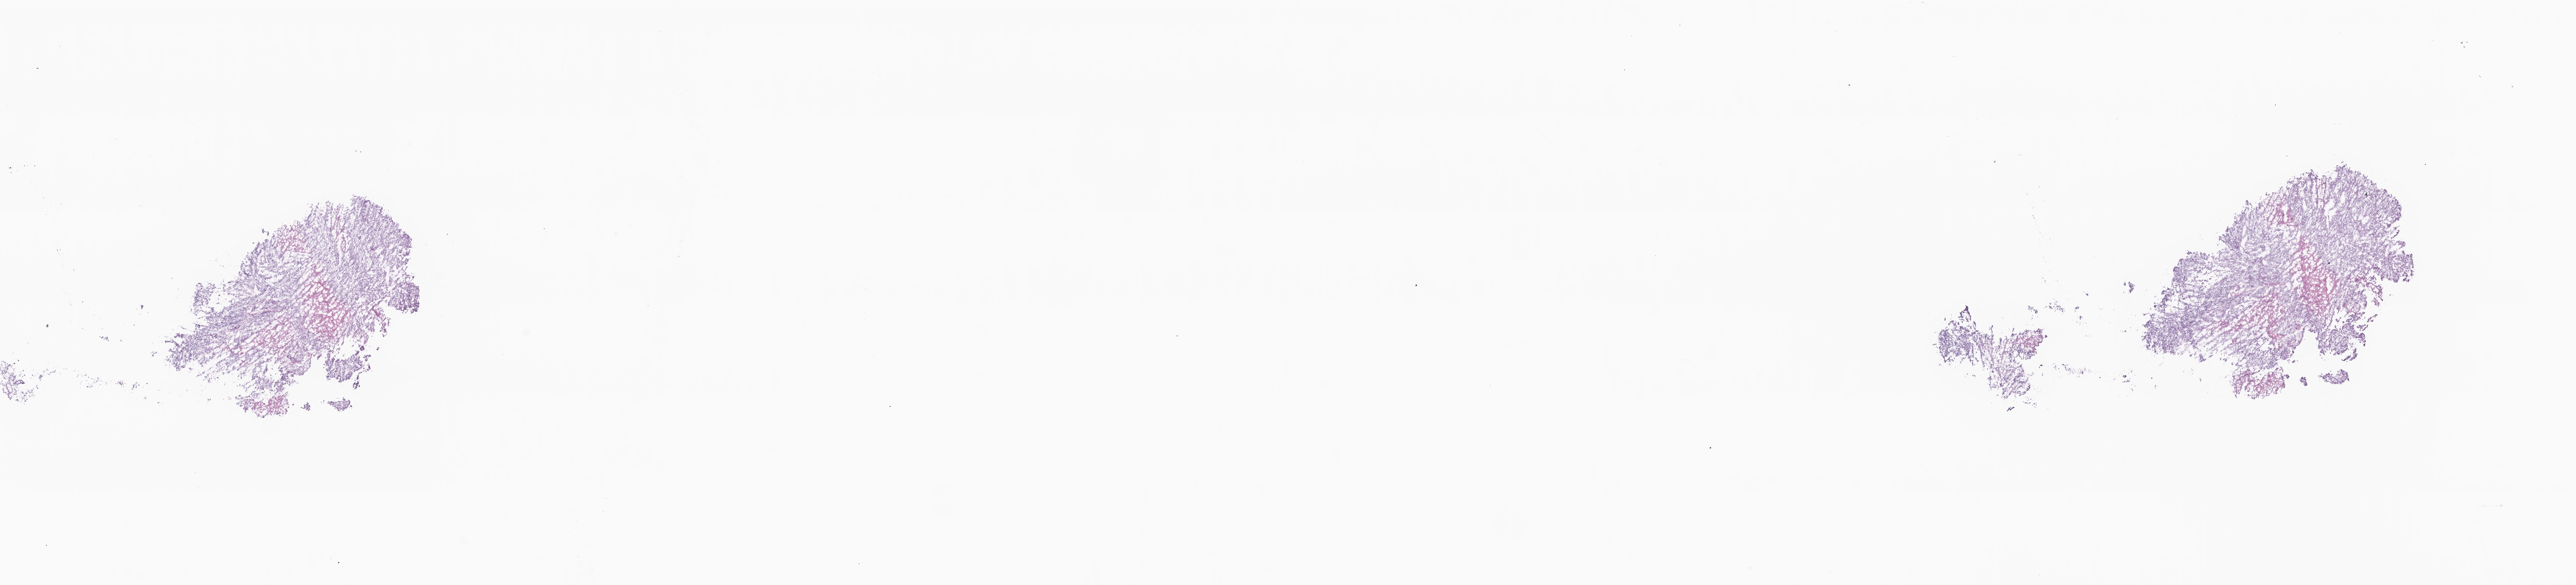
Digitized haematoxylin and eosin-stained section, a low-resolution overview of the entire scanned area, about 29.3 x 6.7 mm, frozen section (tissue freezing medium), primary tumor, site: breast (left). Patient: female, age at initial diagnosis 45 years. Pathologist review of this section (percent, as recorded): tumor cells 80%, tumor nuclei 90%, stromal cells 10%, necrosis 10%, normal cells 0%. Inflammatory infiltration, as recorded: lymphocyte infiltration 0%, monocyte infiltration 0%, neutrophil infiltration 0%.
Section: bottom of the tissue portion. Diagnosis: Infiltrating duct carcinoma, NOS.